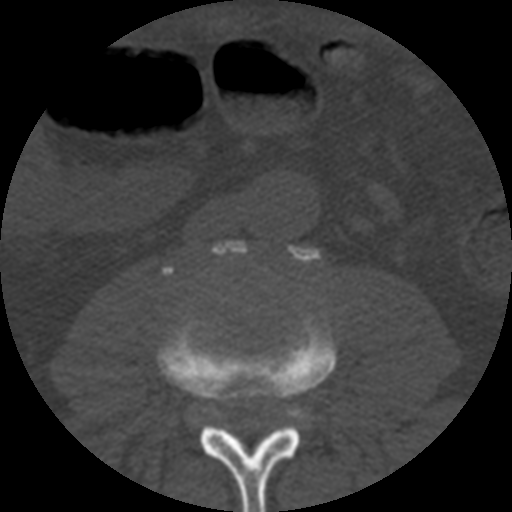
CT including the spine, one axial slice; position 111 of 508 along the scan axis; 120 kVp; bone window (W 1800 / L 400 HU); 512 × 512 image matrix. Patient age 57 years. Case-level facts recorded for this patient, not image findings: primary cancer: prostate.
Structures marked on this image (semi-automatically segmented with operator editing):
- L3 vertebra: bounding box <158,314,337,512> (left, top, right, bottom; pixels)
- L4 vertebra: <213,240,321,427>